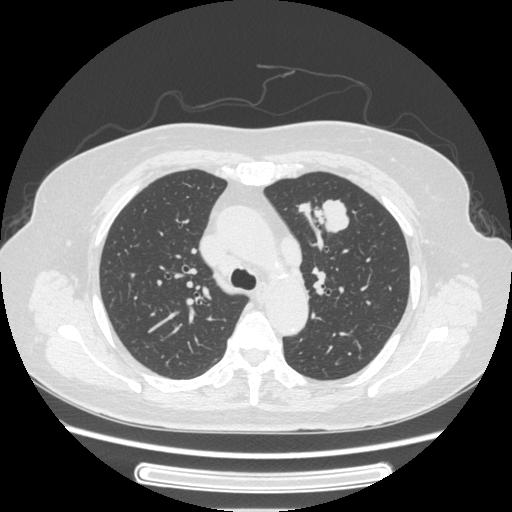
Chest CT, one axial slice. Slice 168 of 227 in the series (ordered by position). 120 kVp. Lung window (W 1500 / L -600 HU). 512 × 512 image matrix, field of view 363 × 363 mm. Female patient, age 77 years. Case-level facts recorded for this patient, not image findings: clinical TNM (as recorded): T1c N3 M0.
Outlined on this slice (bounding box drawn by a radiologist):
- lung tumour (recorded histology: adenocarcinoma): bounding box [x1, y1, x2, y2] px = [297, 193, 351, 252]